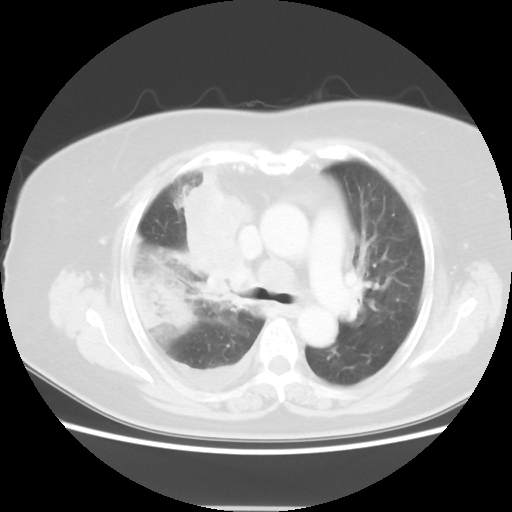
Chest CT, one axial slice. Position 32 of 48 along the scan axis. 120 kVp. Lung window (W 1500 / L -600 HU). 5 mm slice thickness. 512 × 512 image matrix, field of view 360 × 360 mm. Patient: female, 73 years. From the clinical record (not read from this slice): clinical TNM (as recorded): T3 N3 M1b.
Outlined on this slice (bounding box drawn by a radiologist):
- lung tumour (recorded histology: small cell carcinoma): bounding box (x1, y1, x2, y2) in pixels: (175, 168, 264, 289)